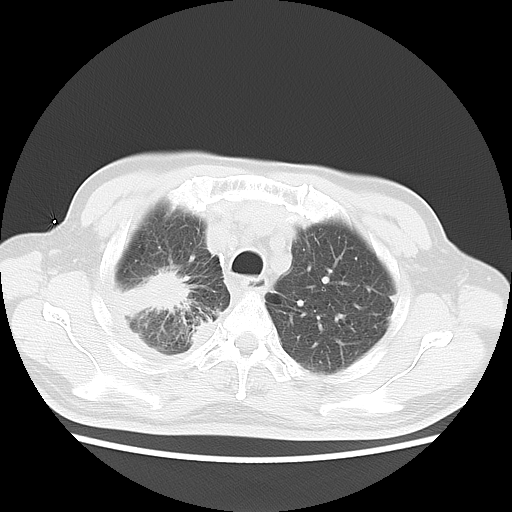
Chest CT, one axial slice; position 14 of 20 along the scan axis; reconstruction kernel LUNG; lung window (W 1500 / L -600 HU); 5 mm slice thickness; 512 × 512 image matrix, field of view 350 × 350 mm. Male patient, age 75 years. Case-level facts recorded for this patient, not image findings: clinical TNM (as recorded): T1c N1 M1.
Structures marked on this image (rectangle marked by the reading radiologist):
- lung tumour (recorded histology: adenocarcinoma): bounding box (x1, y1, x2, y2) in pixels: (122, 259, 191, 318)